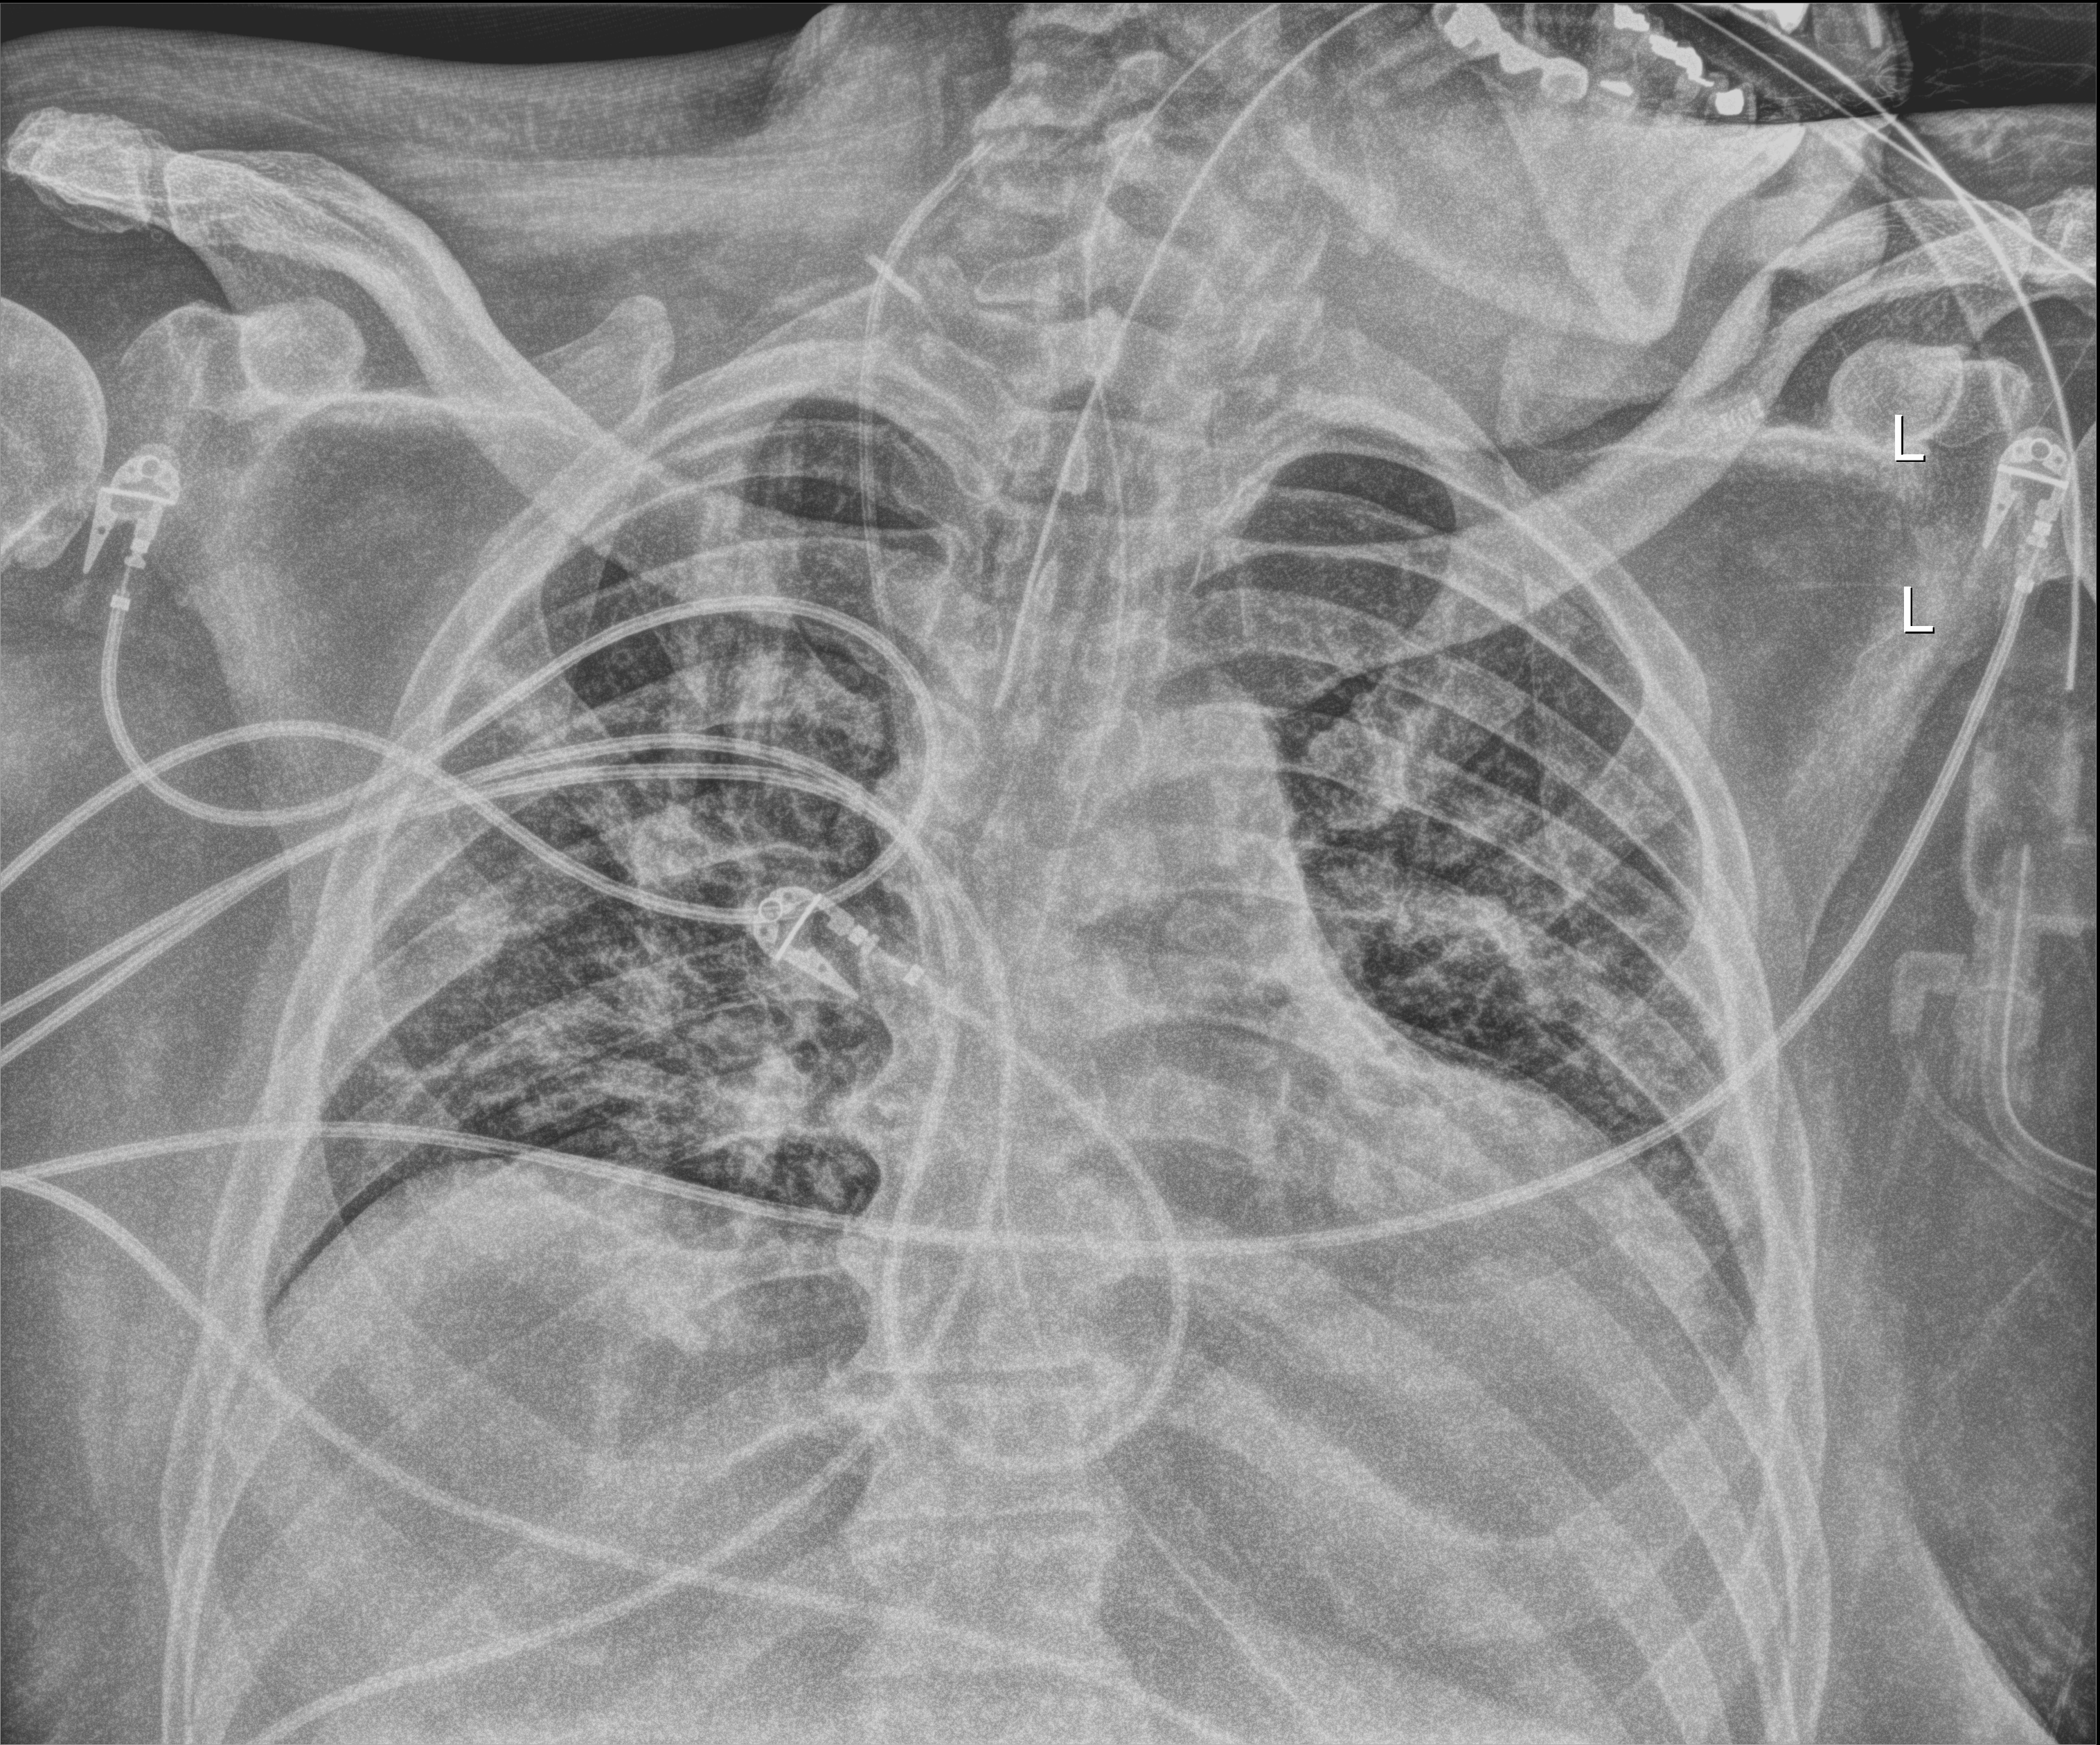
Portable chest radiograph, anteroposterior (AP) projection. Male patient hospitalised with COVID-19, age 18–59 years.
Admission-level facts for this patient (not findings on this image; timing relative to this image not recorded): hypertension (admission record): no; COPD (admission record): no.